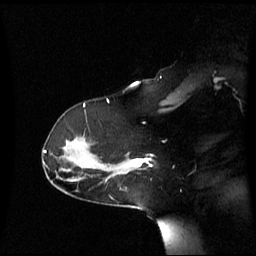
Breast MRI (dynamic contrast-enhanced), one sagittal slice. Slice 42 of 60 in the series (ordered by position). Dynamic contrast-enhanced series, image 2 of 3 at this slice position (ordered by acquisition). 1.5 T. TE 4.2 ms, TR 8.4 ms. 2.6 mm slice thickness. 256 × 256 image matrix, field of view 270 × 270 mm. Patient: female, 39 years. Case-level facts recorded for this patient, not image findings: setting: breast cancer imaged before/during neoadjuvant chemotherapy; receptor status: triple-negative.
Annotated regions visible in this slice (semi-automatic segmentation, software-assisted and operator-edited):
- analysis volume of interest (the breast-tissue region the enhancement analysis was run in; not a lesion): bounding box [x1, y1, x2, y2] px = [117, 153, 152, 175]
- tumour enhancement mask (voxels above the 70 % enhancement threshold inside the analysis volume of interest): [132, 158, 152, 167]